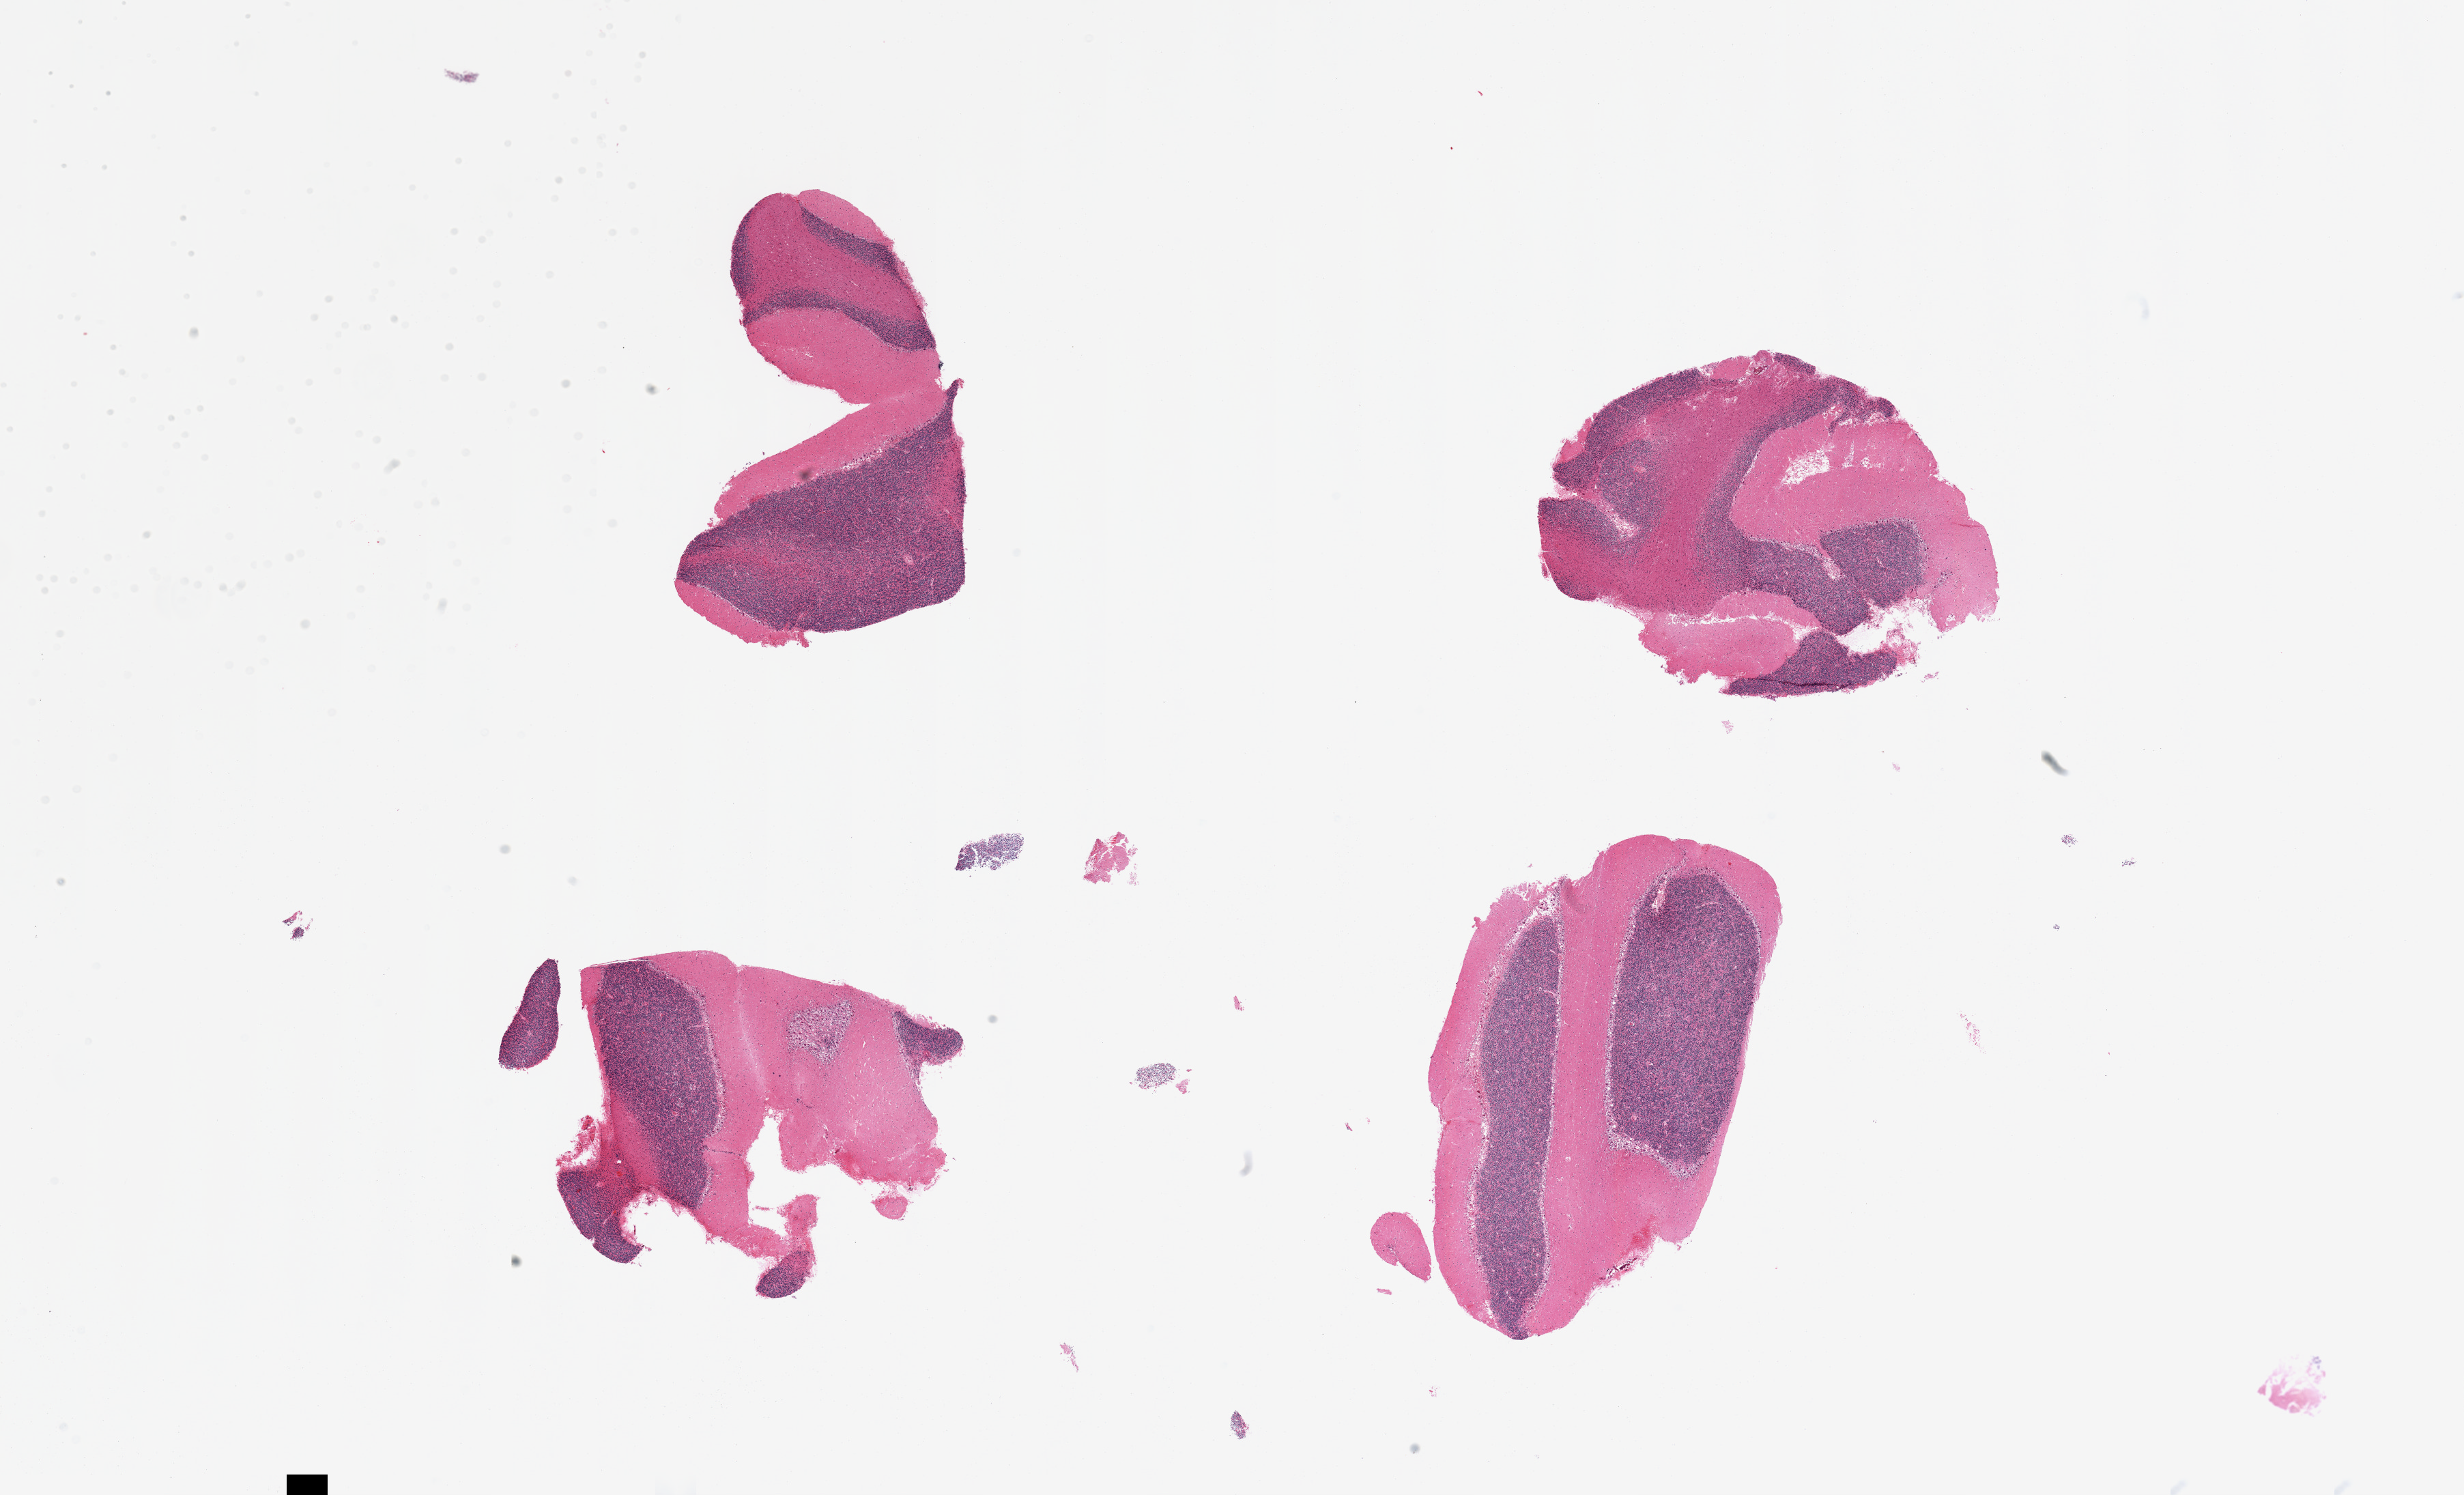
Digitized H&E-stained section, low-resolution overview of the scanned area, about 28.5 x 17.3 mm (from a 20x scan), PAXgene-fixed paraffin-embedded (PFPE) section, section of cerebellum (target tissue), tissue donor sample. Donor sex: male.
Review note (as recorded): 4 pieces.